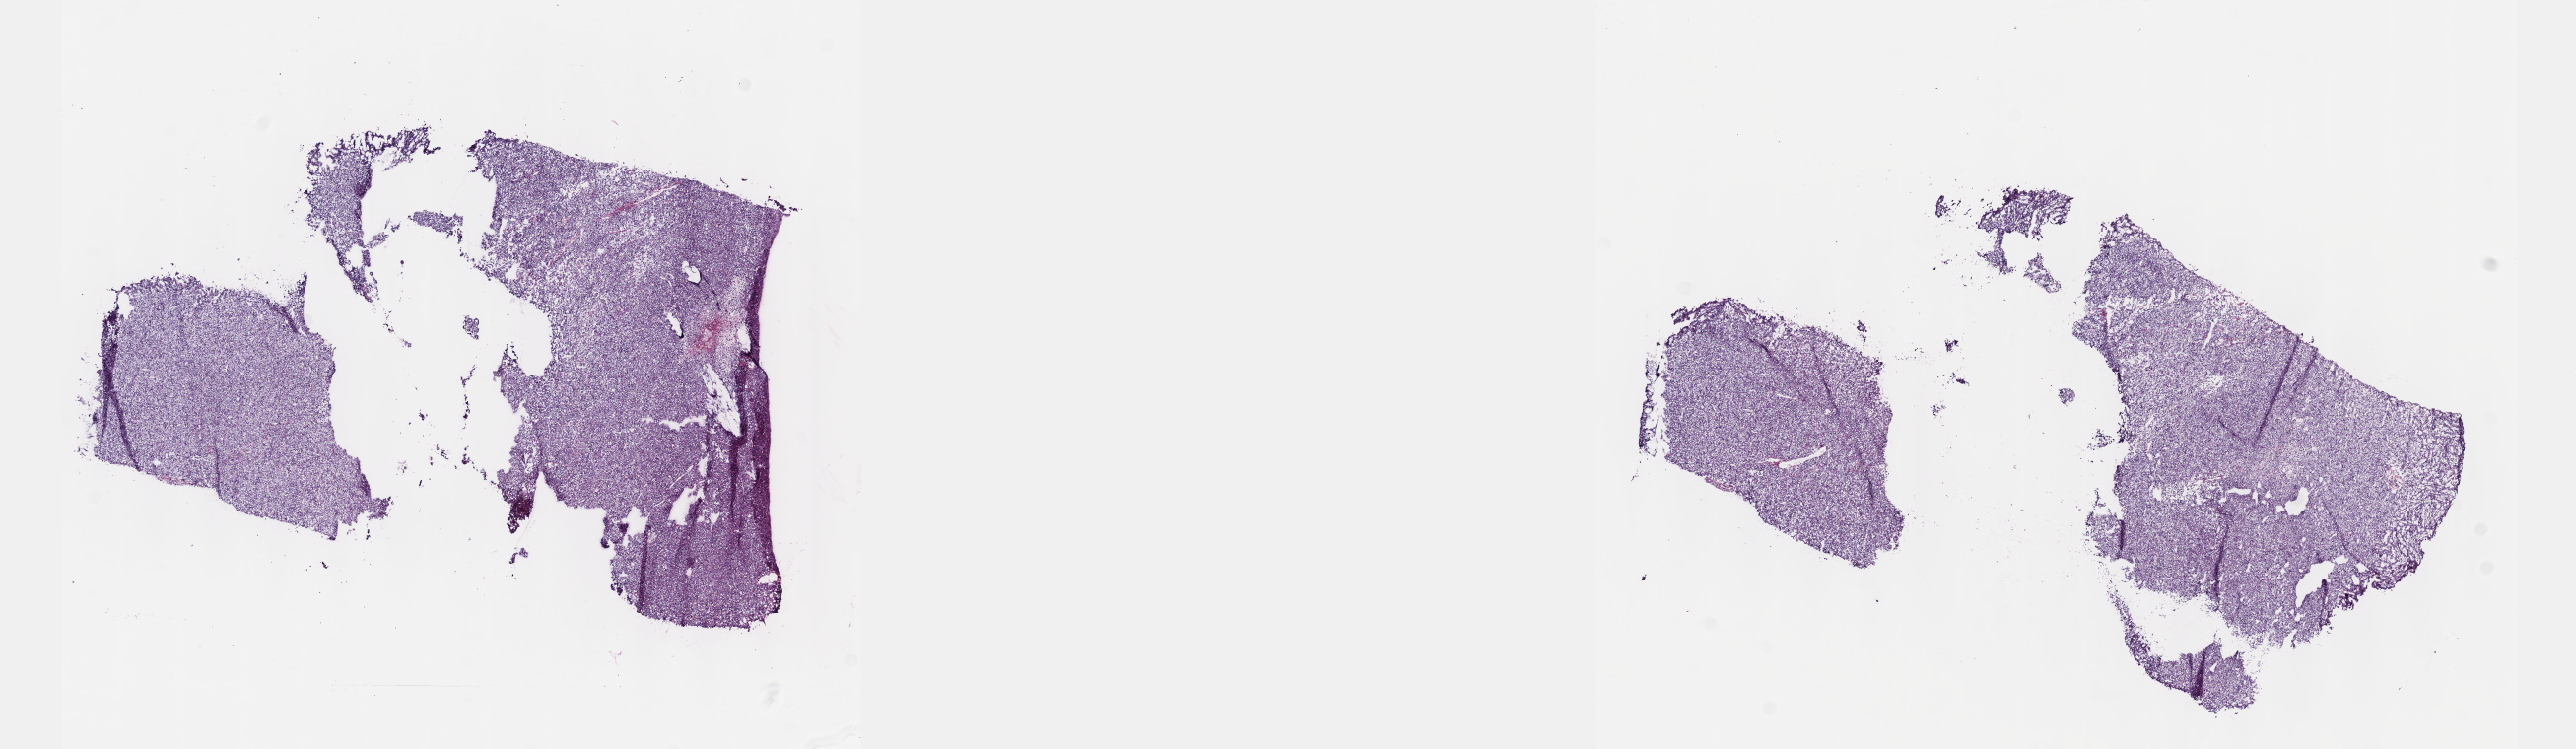
Digitized H&E-stained tissue section (whole slide) — whole scanned area (about 21.1 x 6.1 mm, acquisition: 40x scan) shown as a low-resolution overview; frozen section from the top of the tissue portion; primary tumour sample from the thymus. Male patient; age at initial diagnosis 69 years.
Histologic diagnosis: Thymoma, type A, malignant (anterior mediastinum).